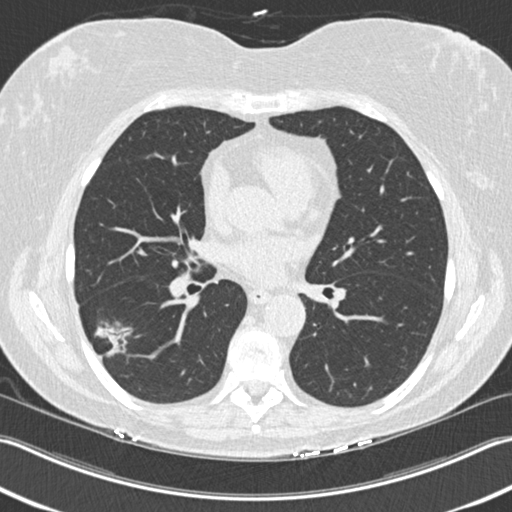
Axial slice from a low-dose chest CT screening exam. Baseline annual screen. Lung window (W 1500 / L -600 HU). Standard (soft-tissue) reconstruction kernel (B30f). Slice 94 of 211 in the series. 512 × 512 image matrix, field of view 348 × 348 mm. Female participant, aged 63 years at enrolment. Current smoker at enrolment.
Lesion marked by an expert reader, bounding box (x1, y1, x2, y2) in pixels: (79, 316, 140, 372). The screening reader recorded 3 non-calcified nodules or masses ≥4 mm on this exam; which of them this box marks is not recorded. Later outcome: lung cancer diagnosed 57 days after this screen — bronchiolo-alveolar adenocarcinoma, NOS, right lower lobe, well differentiated (G1), stage IA (AJCC 6th edition), 25 mm at pathology.